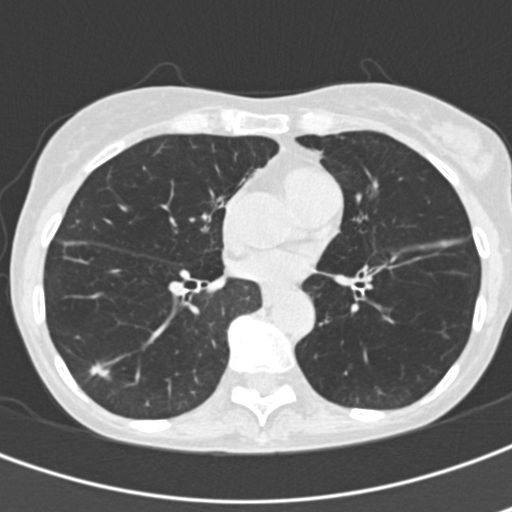
Axial slice from a low-dose chest CT screening exam; second annual screen; lung window (W 1500 / L -600 HU); 2 mm slice thickness; 120 kVp; slice 101 of 201 in the series; 512 × 512 image matrix. Female, age 68 years at enrolment. Former smoker at enrolment.
Expert reader's lesion annotation, bounding box (x1, y1, x2, y2) in pixels: (76, 352, 118, 389). Screening reader's record for this exam (one nodule recorded; not confirmed to be the boxed lesion): non-calcified nodule or mass ≥4 mm, right lower lobe, 9 × 7 mm, spiculated (stellate) margins, soft tissue attenuation, pre-existing on the prior screen: yes; interval growth: yes. Participant outcome: lung cancer diagnosed 659 days after this screen — squamous cell carcinoma, NOS, right lower lobe, stage IA (AJCC 6th edition).